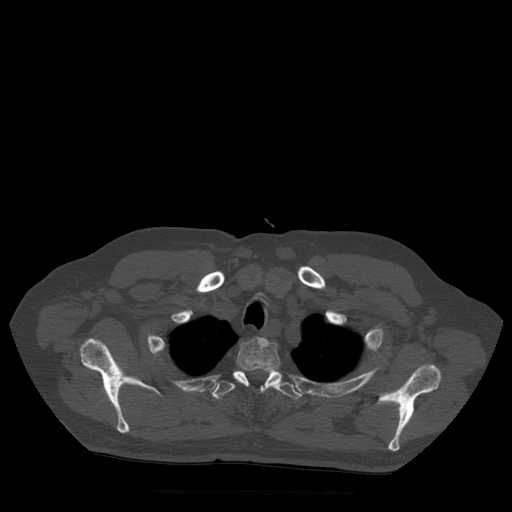
CT including the spine, one axial slice. Slice 417 of 522 in the series (ordered by position). Bone window (W 1800 / L 400 HU). 1.25 mm slice thickness. 512 × 512 image matrix, field of view 420 × 420 mm. Patient age 72 years. Case-level facts recorded for this patient, not image findings: primary cancer: prostate.
Annotated regions visible in this slice (semi-automatic segmentation, software-assisted and operator-edited):
- T2 vertebra: bounding box [x1, y1, x2, y2] px = [233, 337, 282, 392]
- T3 vertebra: [212, 370, 302, 400]